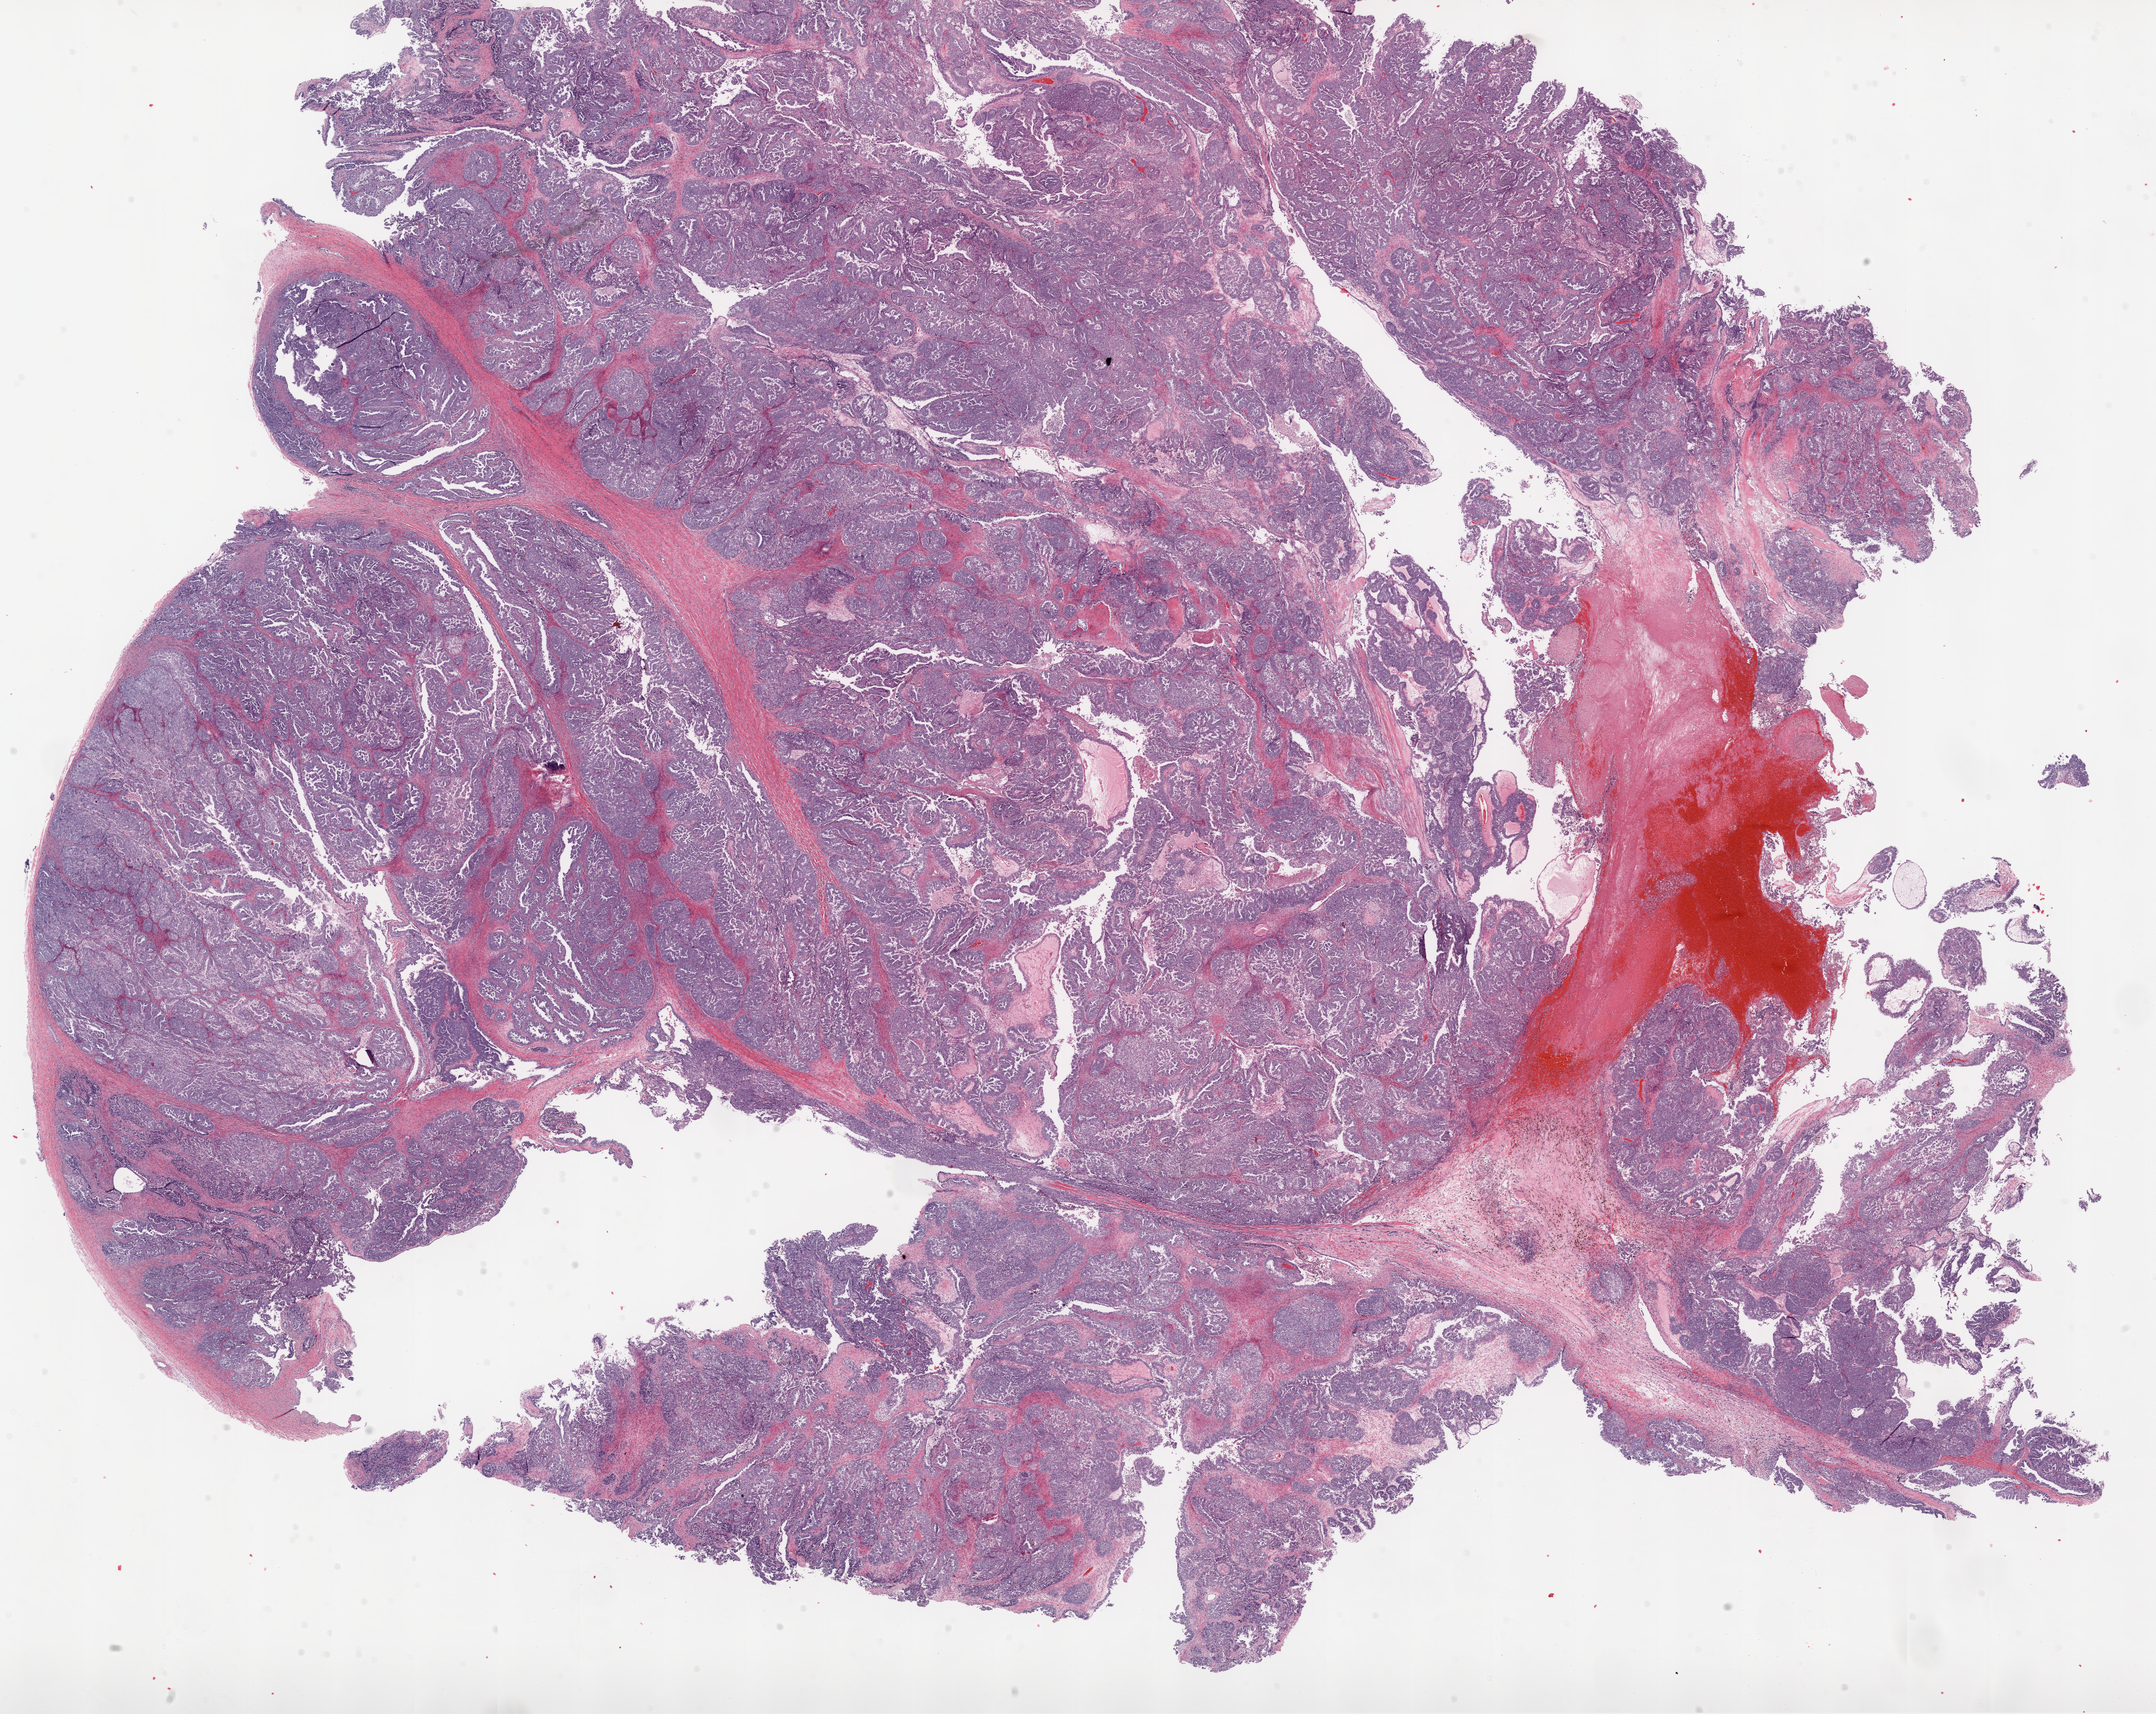
H&E whole-slide image — a low-resolution overview of the entire scanned area, about 26.1 x 20.7 mm (slide scanned at 20x). Frozen section from the top of the tissue portion. Ovary, primary tumour sample. Female, age 54 years at initial diagnosis. Histologic grade: G3 (poorly differentiated). Slide review estimates, as recorded: tumour cells 83%, tumour nuclei 85%, normal cells 0%, stromal cells 12%, necrosis 5%.
• FIGO stage: IIC
• diagnosis: Serous cystadenocarcinoma, NOS